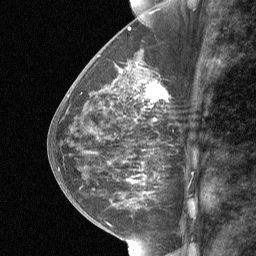
Breast MRI (dynamic contrast-enhanced), one sagittal slice; slice 30 of 64 in the series (ordered by position); dynamic contrast-enhanced study with each time point stored as its own series, time point 2 of 3 at this slice position (early post-contrast, ordered by acquisition time); 1.5 T; TE 4.8 ms, TR 27 ms; 256 × 256 image matrix. Patient: female, 59 years. Case-level facts recorded for this patient, not image findings: setting: breast cancer imaged before/during neoadjuvant chemotherapy; receptor status: triple-negative.
Annotated regions visible in this slice (semi-automatically segmented with operator editing):
- analysis volume of interest (the breast-tissue region the enhancement analysis was run in; not a lesion): bounding box (x1, y1, x2, y2) in pixels: (127, 66, 167, 122)
- tumour enhancement mask (voxels above the 90 % enhancement threshold inside the analysis volume of interest): (146, 83, 165, 102)